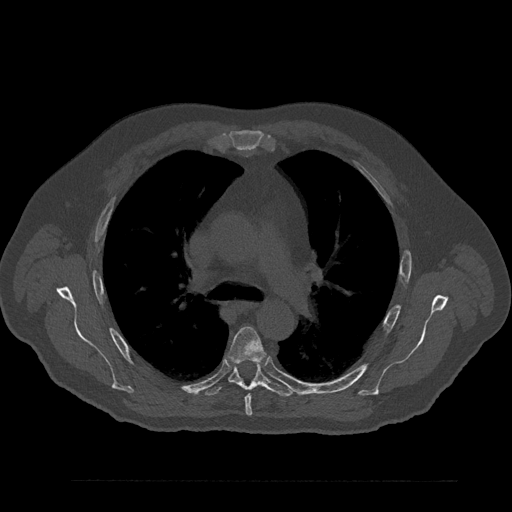
CT including the spine, one axial slice. Slice 580 of 797 in the series (ordered by position). Reconstruction kernel Br40s/3. Bone window (W 1800 / L 400 HU). 0.5 mm slice thickness. 512 × 512 image matrix, field of view 430 × 430 mm. Male patient, age 61 years. From the clinical record (not read from this slice): primary cancer: prostate.
Annotated regions visible in this slice (semi-automatic segmentation, software-assisted and operator-edited):
- T5 vertebra: box from (x=228, y=327) to (x=266, y=416) px
- T6 vertebra: (x=204, y=361)–(x=293, y=397)